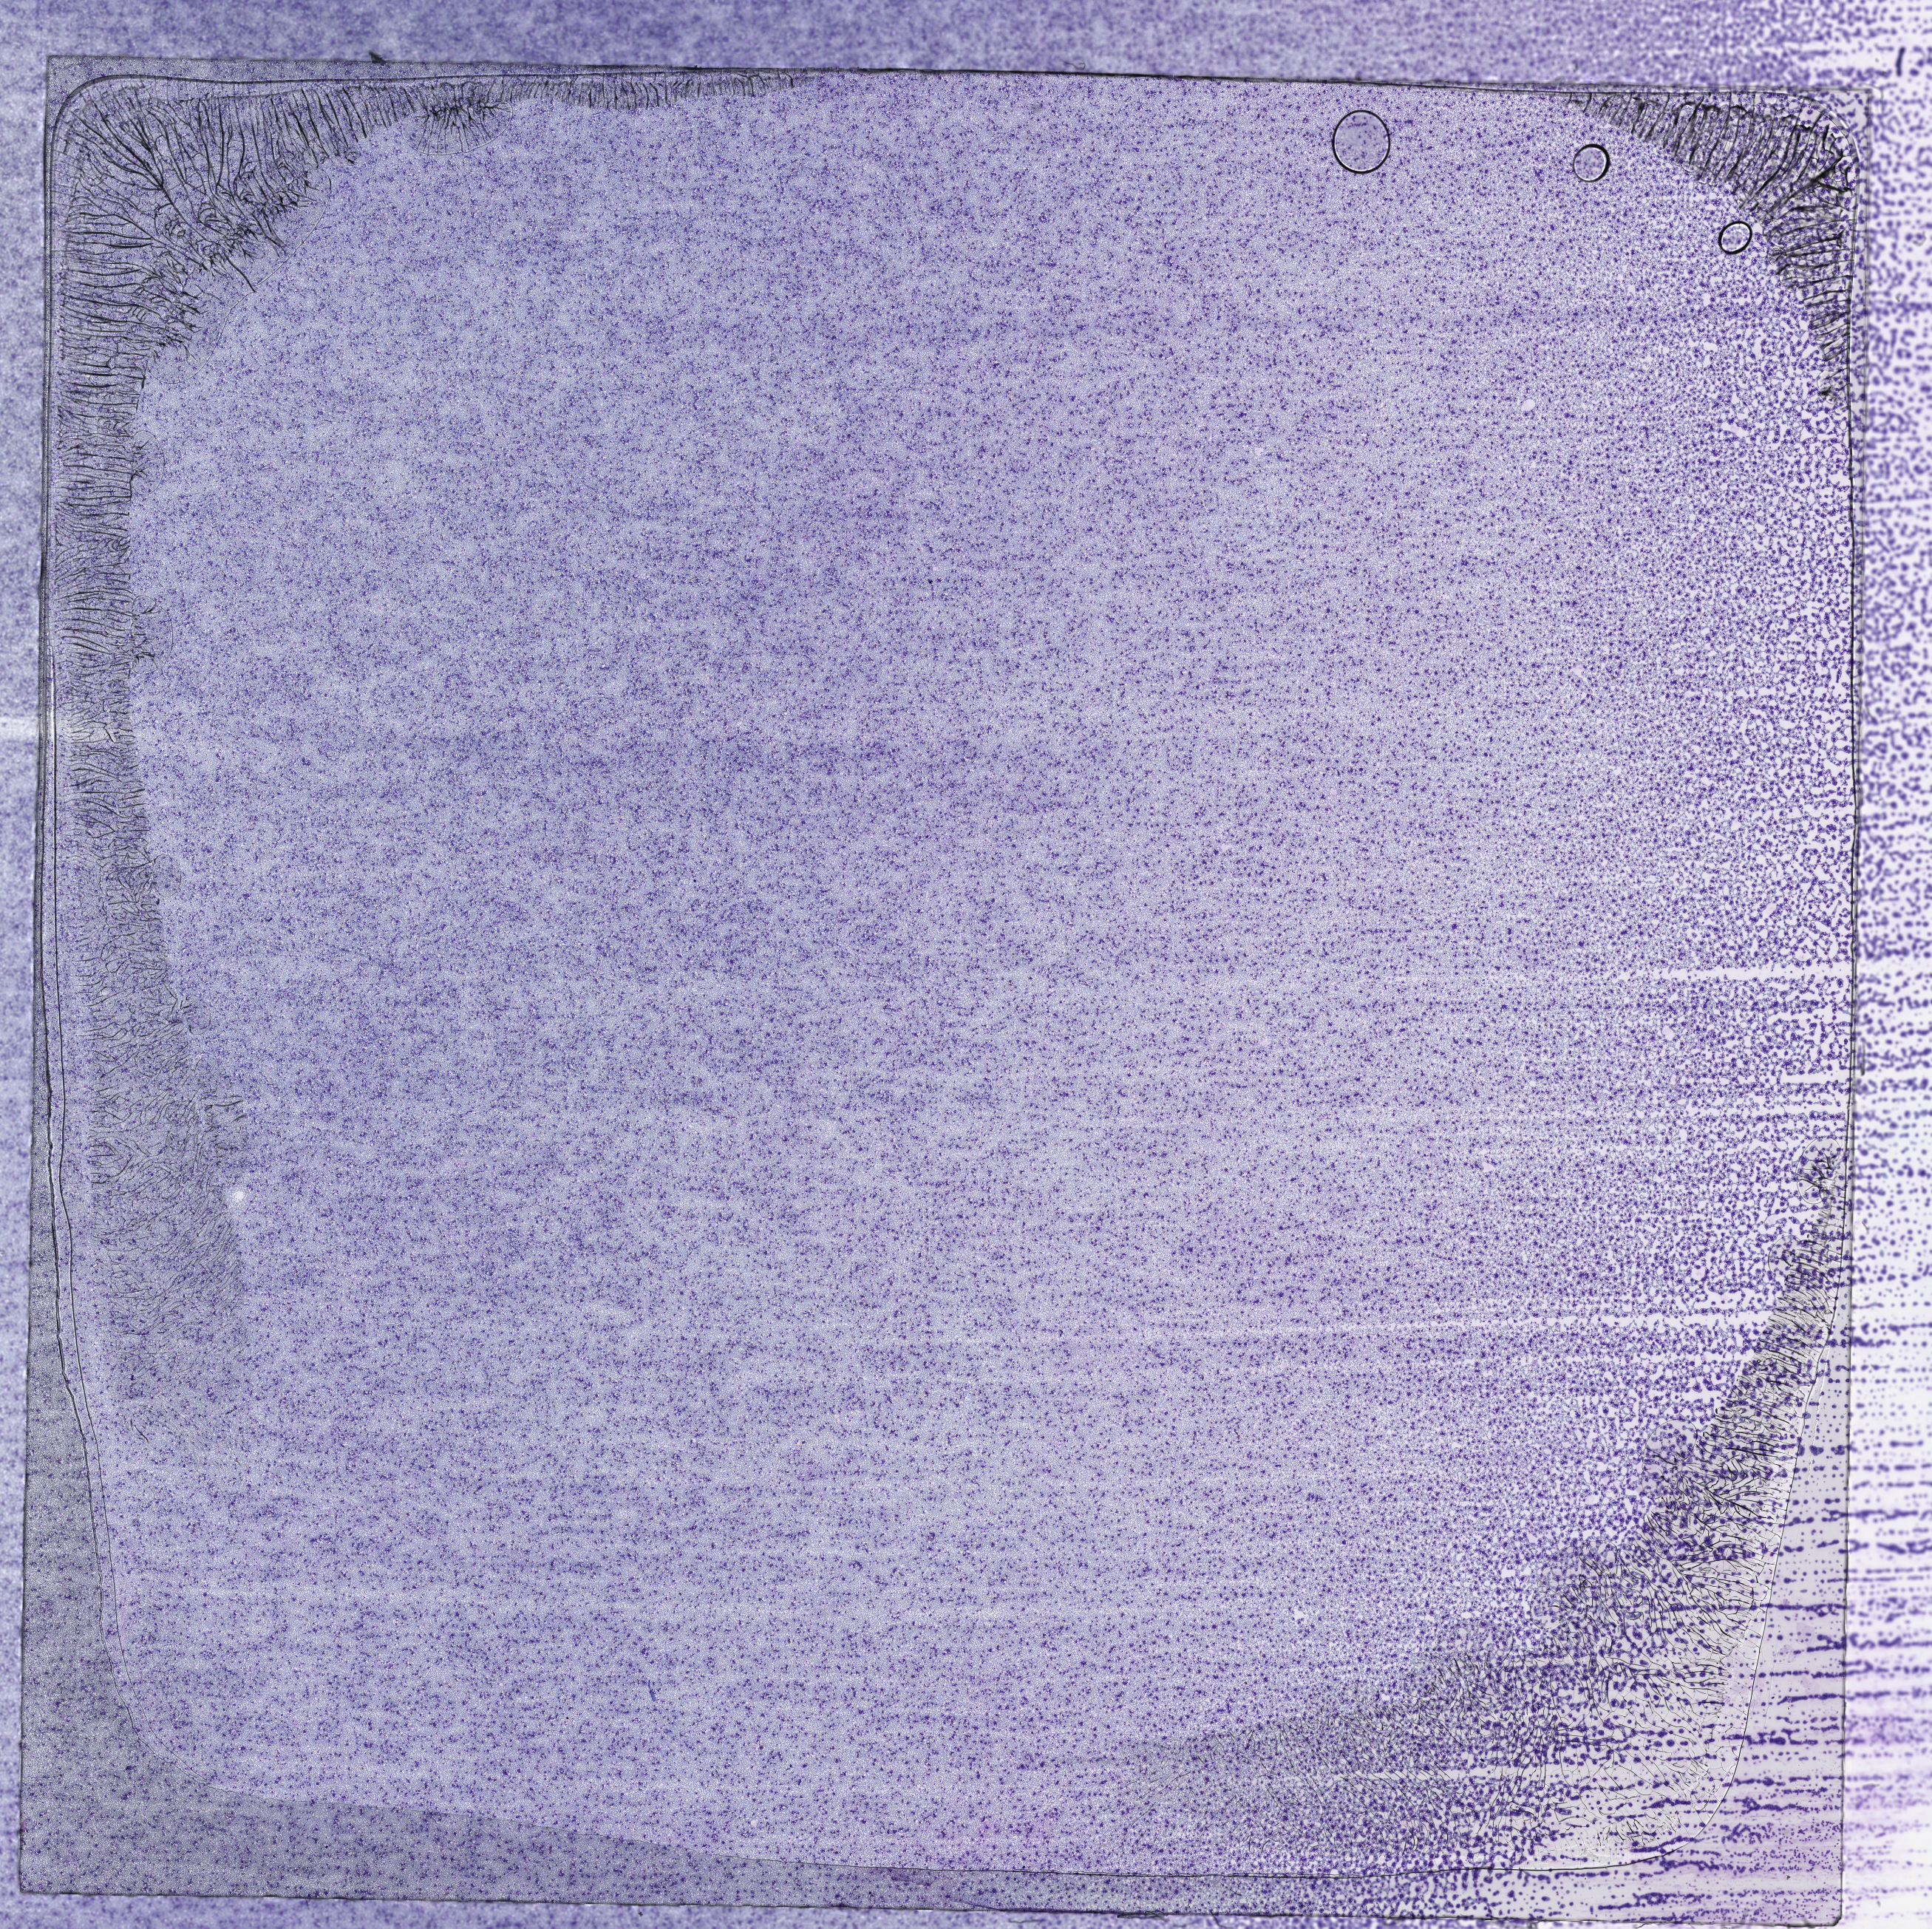
Whole-slide histology image, Hematoxylin and eosin (H&E) stained — shown as a low-resolution overview of the whole scanned area (about 21.1 x 21.1 mm); peripheral blood (leukaemic) sample. Patient: male, age 54 years.
Diagnosis: Acute Myeloid Leukemia.